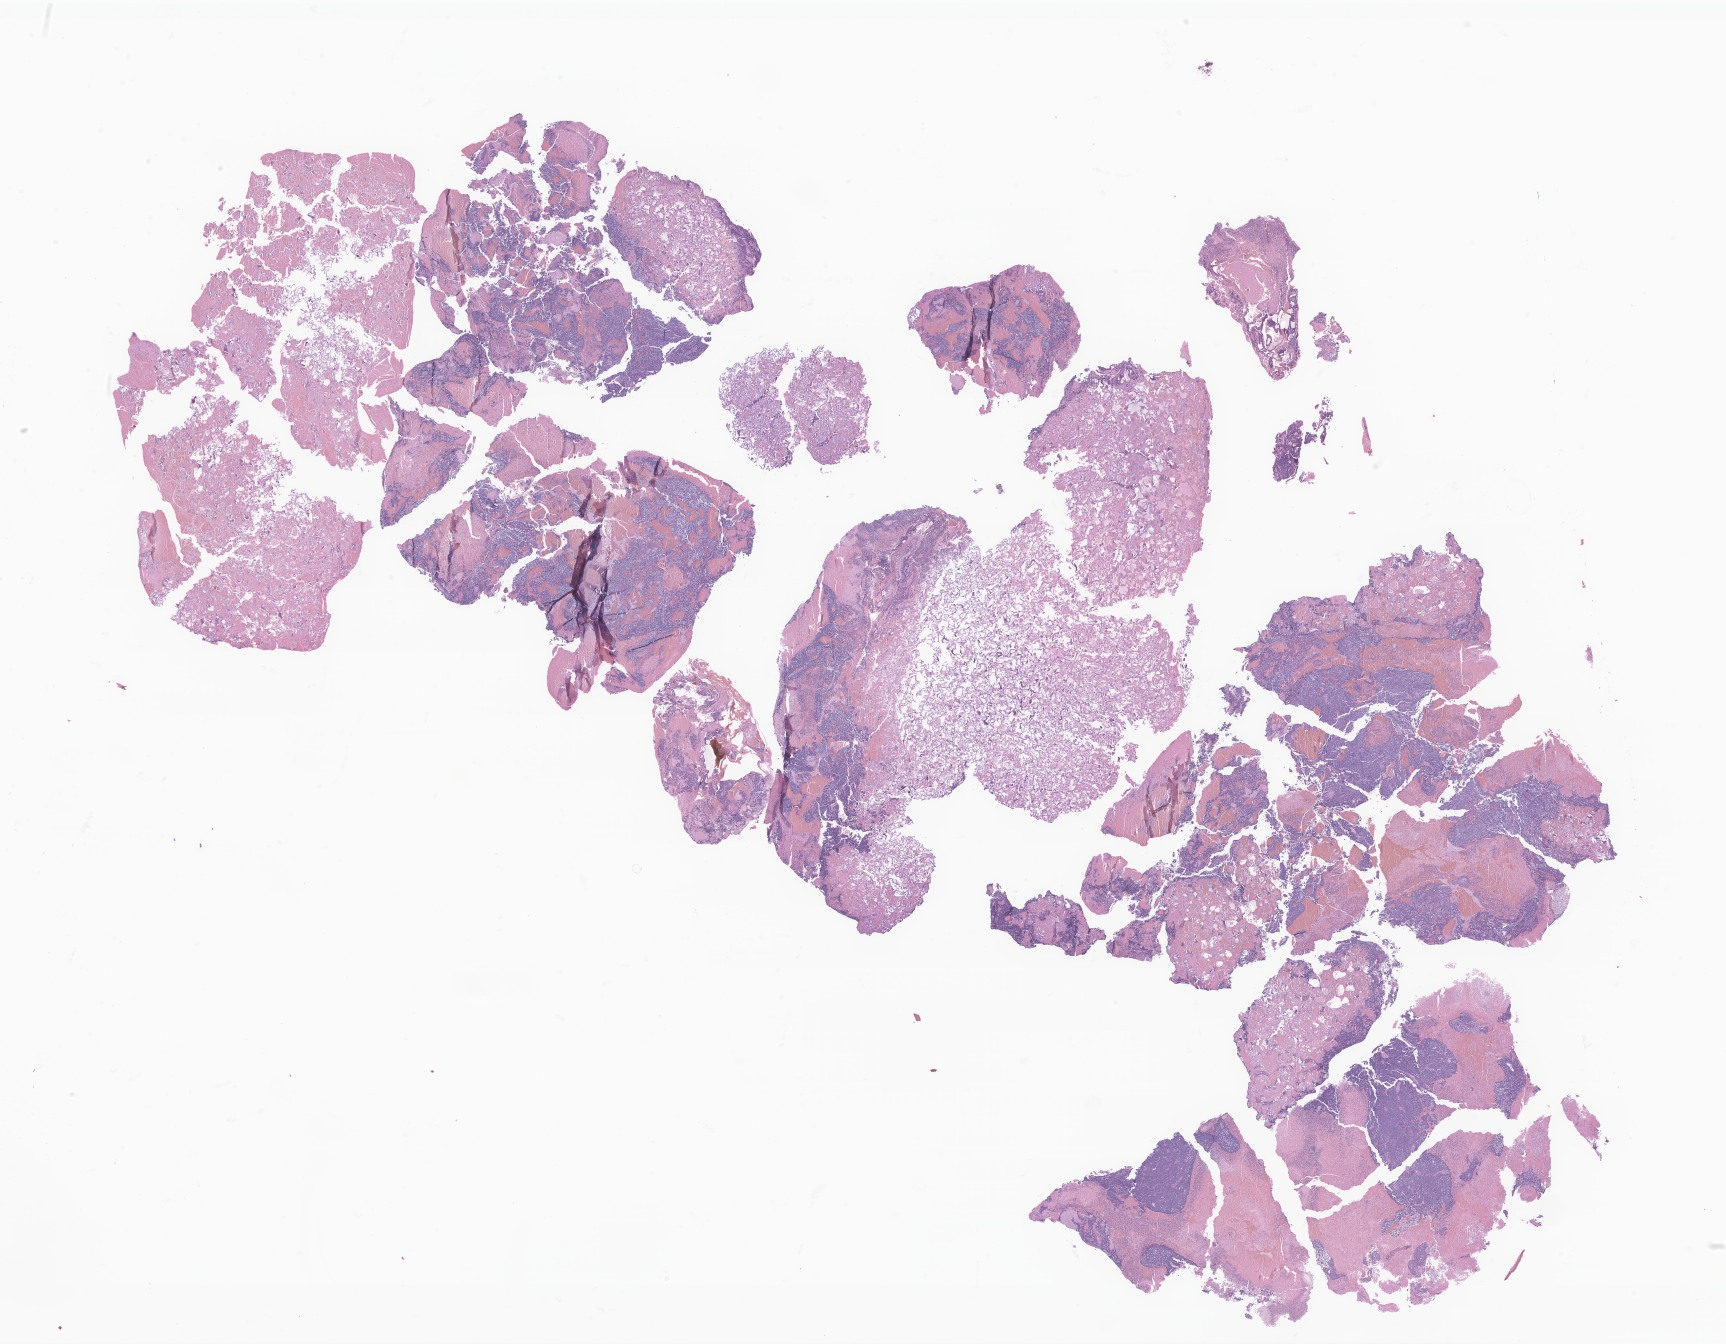
Whole-slide image, haematoxylin and eosin stain of tumor tissue from the brain — low-resolution overview of the scanned area, about 29.1 x 22.7 mm; FFPE section. Male patient, age 38 months (3 years 2 months).
- diagnosis (ICD-O-3 morphology term): Medulloblastoma, NOS